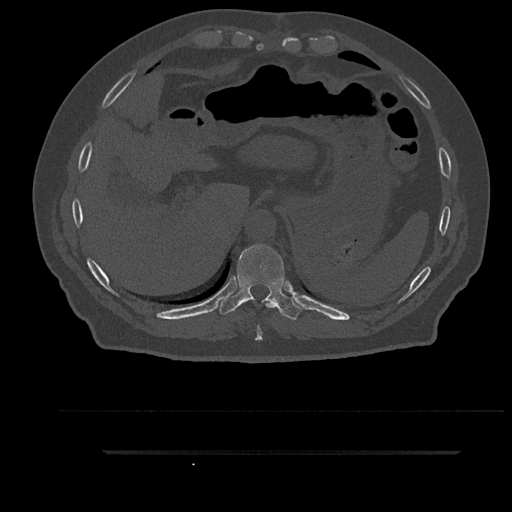
CT including the spine, one axial slice. Position 383 of 797 along the scan axis. 120 kVp. Bone window (W 1800 / L 400 HU). 512 × 512 image matrix, field of view 432 × 432 mm. Patient: male, 63 years. From the clinical record (not read from this slice): primary cancer: renal.
Structures marked on this image (semi-automatically segmented with operator editing):
- T10 vertebra: bounding box [x1, y1, x2, y2] px = [219, 244, 303, 320]
- T9 vertebra: [255, 300, 275, 341]